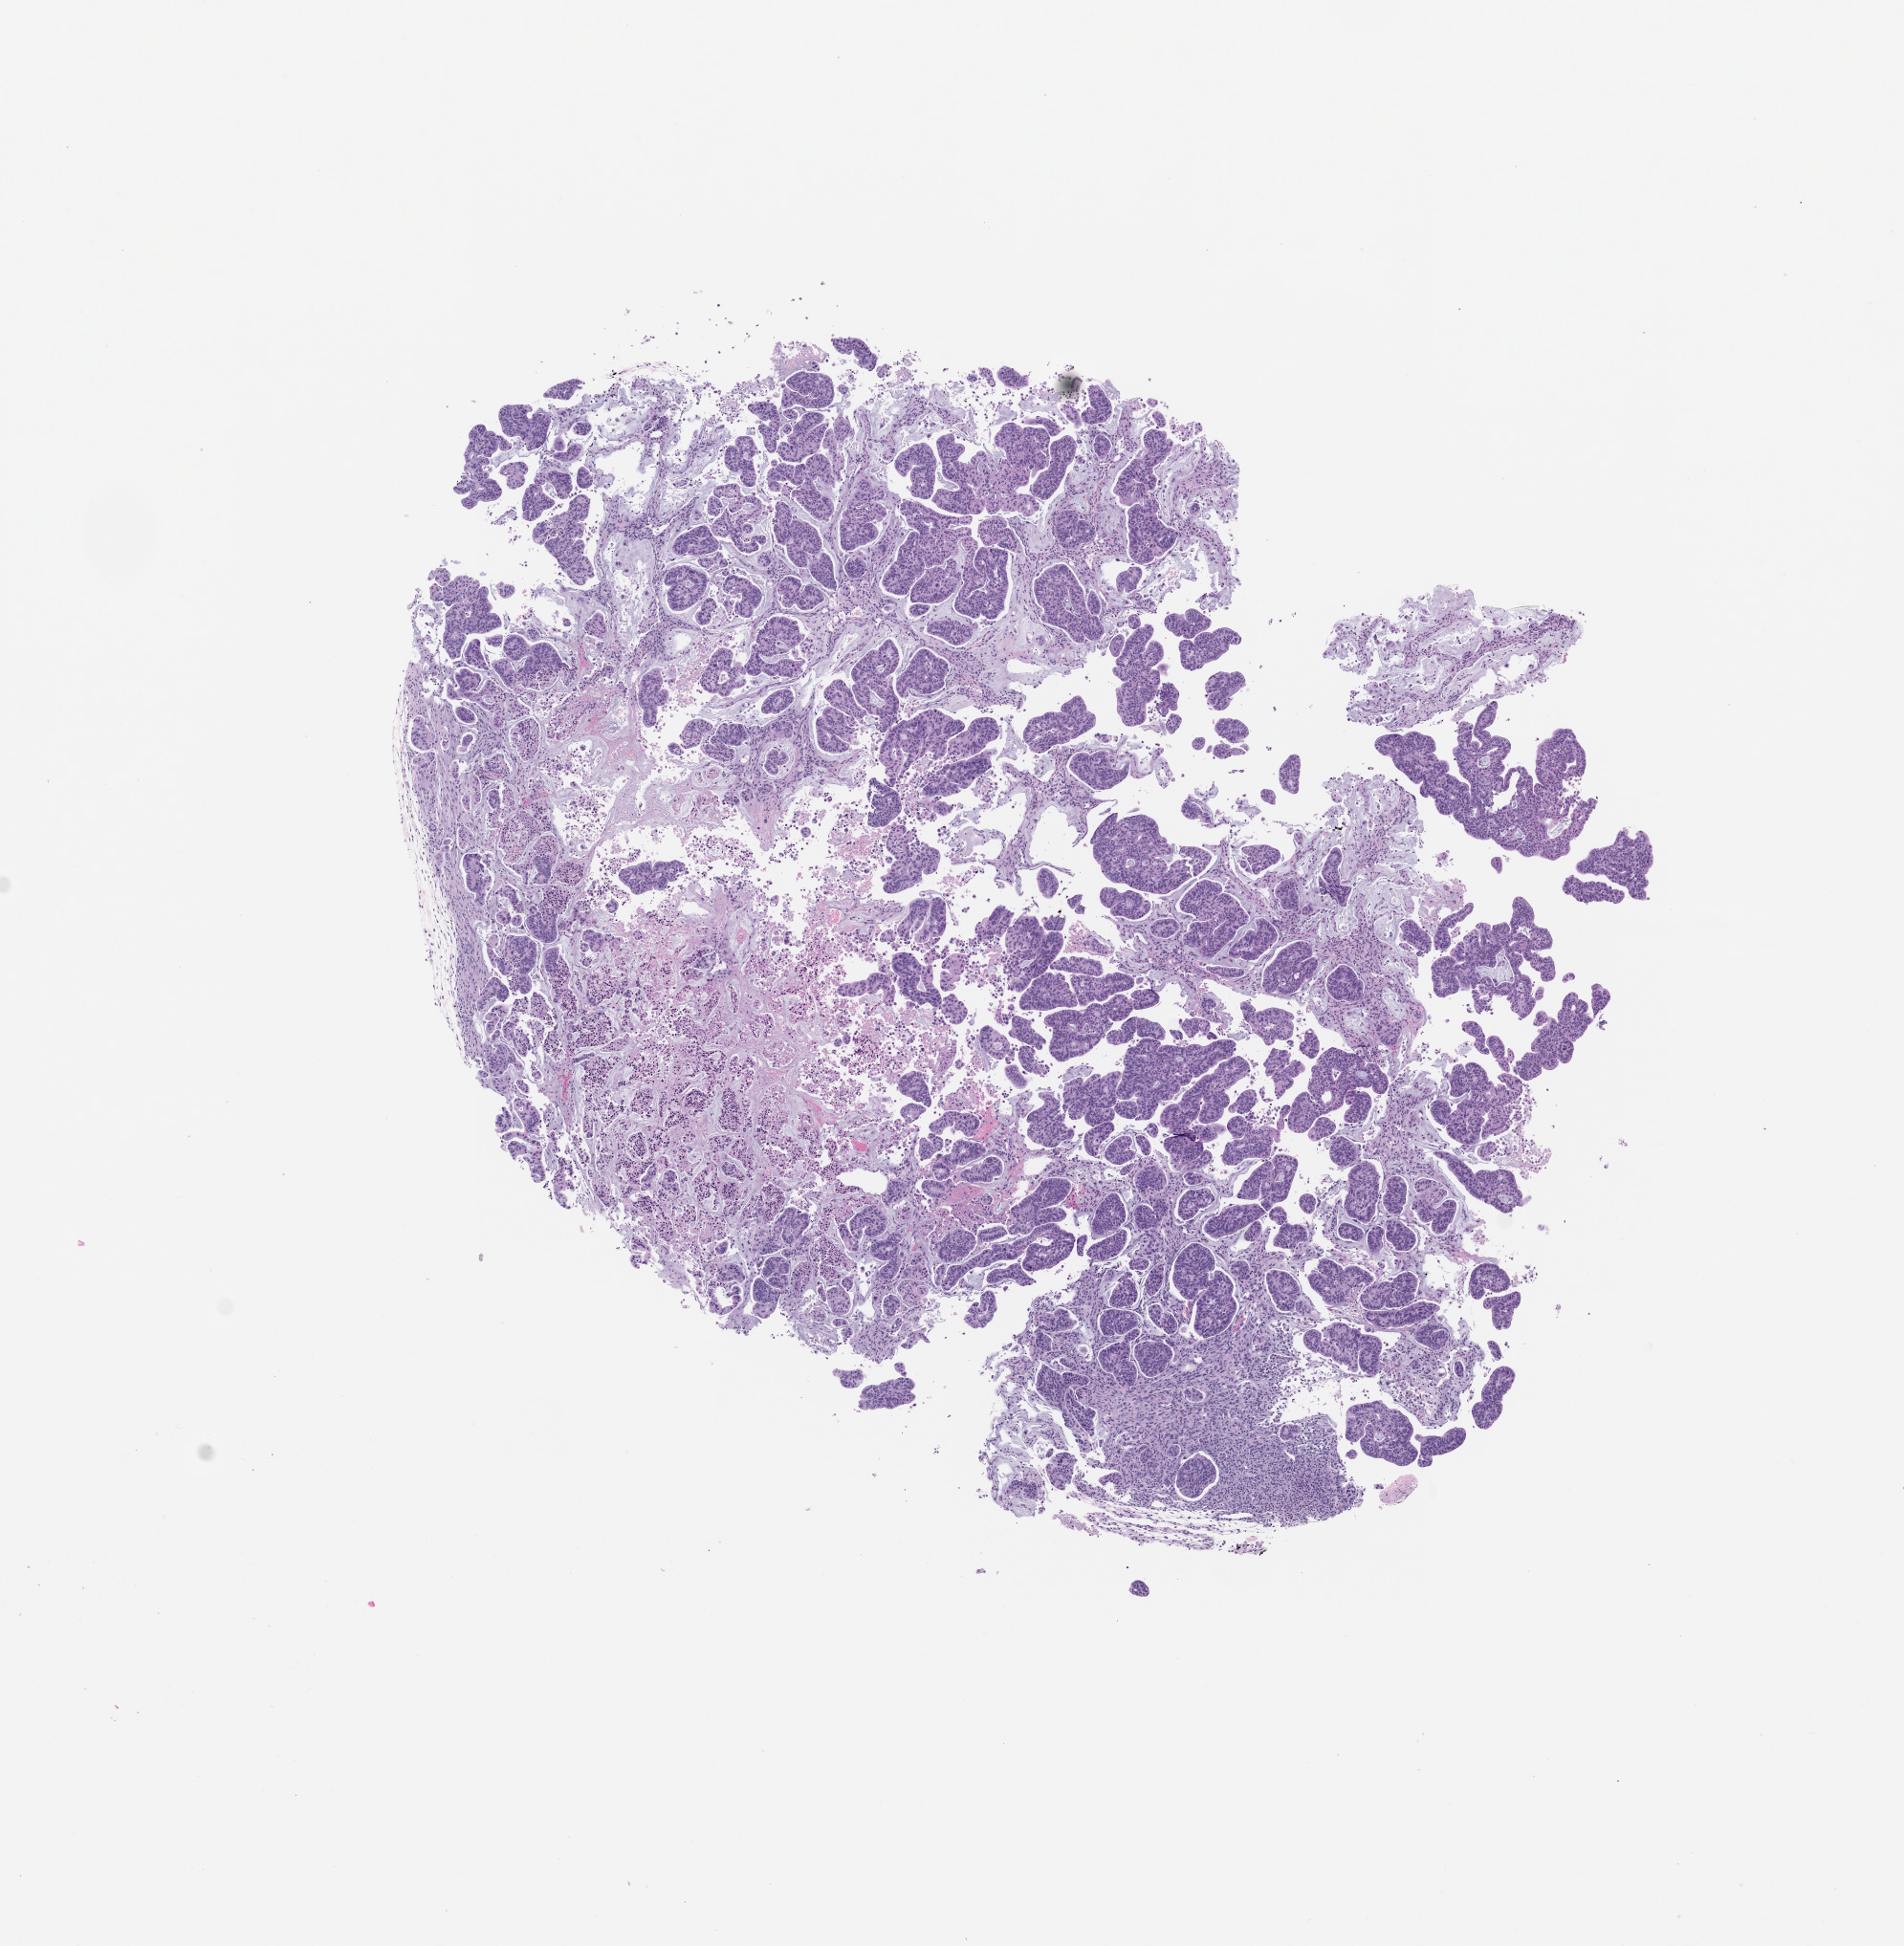
Whole-slide image, hematoxylin and eosin (H&E): patient-derived xenograft (human tumor grown in a mouse), passage 0, low-resolution overview of the scanned area, about 8.0 x 8.2 mm. Formalin-fixed, paraffin-embedded (FFPE) tissue. Tumor site category: small intestine.
* originating patient diagnosis: Small Intestinal Adenocarcinoma